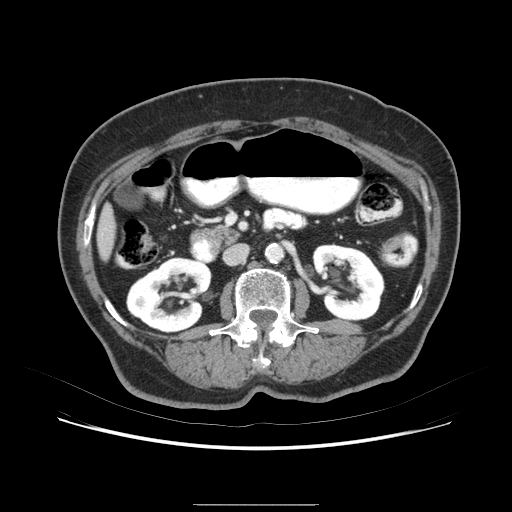
Contrast-enhanced abdominal CT (liver protocol), one axial slice. Slice 22 of 79 in the series (ordered by position). 120 kVp. Soft-tissue window (W 400 / L 40 HU). 2.5 mm slice thickness. 512 × 512 image matrix, field of view 380 × 380 mm. From the clinical record (not read from this slice): diagnosis: hepatocellular carcinoma (patient treated with transarterial chemoembolisation; whether this scan precedes or follows treatment is not stated here); TNM stage (as recorded): Stage-I; Child-Pugh class: A; tumour differentiation: poorly differentiated.
Outlined on this slice (semi-automatically segmented with operator editing):
- liver parenchyma outside the tumour (the mass and vessels are separate outlines, so this box may not span the whole liver): bounding box (x1, y1, x2, y2) in pixels: (94, 161, 148, 282)
- liver vessels: (114, 246, 116, 248)